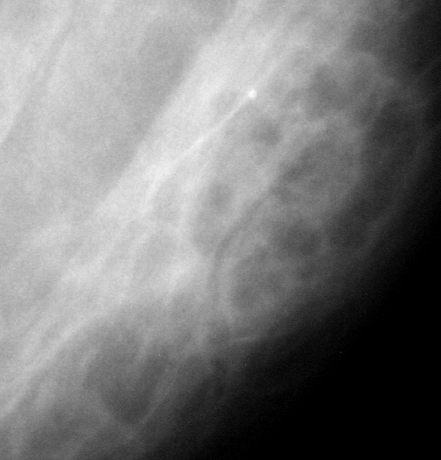
Region of interest cut from a scanned film mammogram (one marked finding); left breast; CC view.
Mass, shape focal asymmetric density, margins ill defined; BI-RADS assessment category 3; pathology result (as recorded, not read from the image): benign.